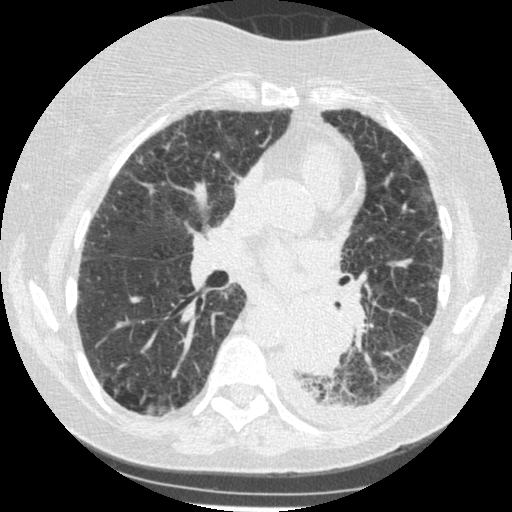
Low-dose screening chest CT, one axial slice; position 129 of 341 along the scan axis; lung window (W 1500 / L -600 HU); 512 × 512 image matrix, field of view 310 × 310 mm.
Annotated regions visible in this slice (manually delineated by an expert):
- lesion 1 (tumor, lower lobe of left lung): bounding box (x1, y1, x2, y2) in pixels: (285, 304, 347, 375)